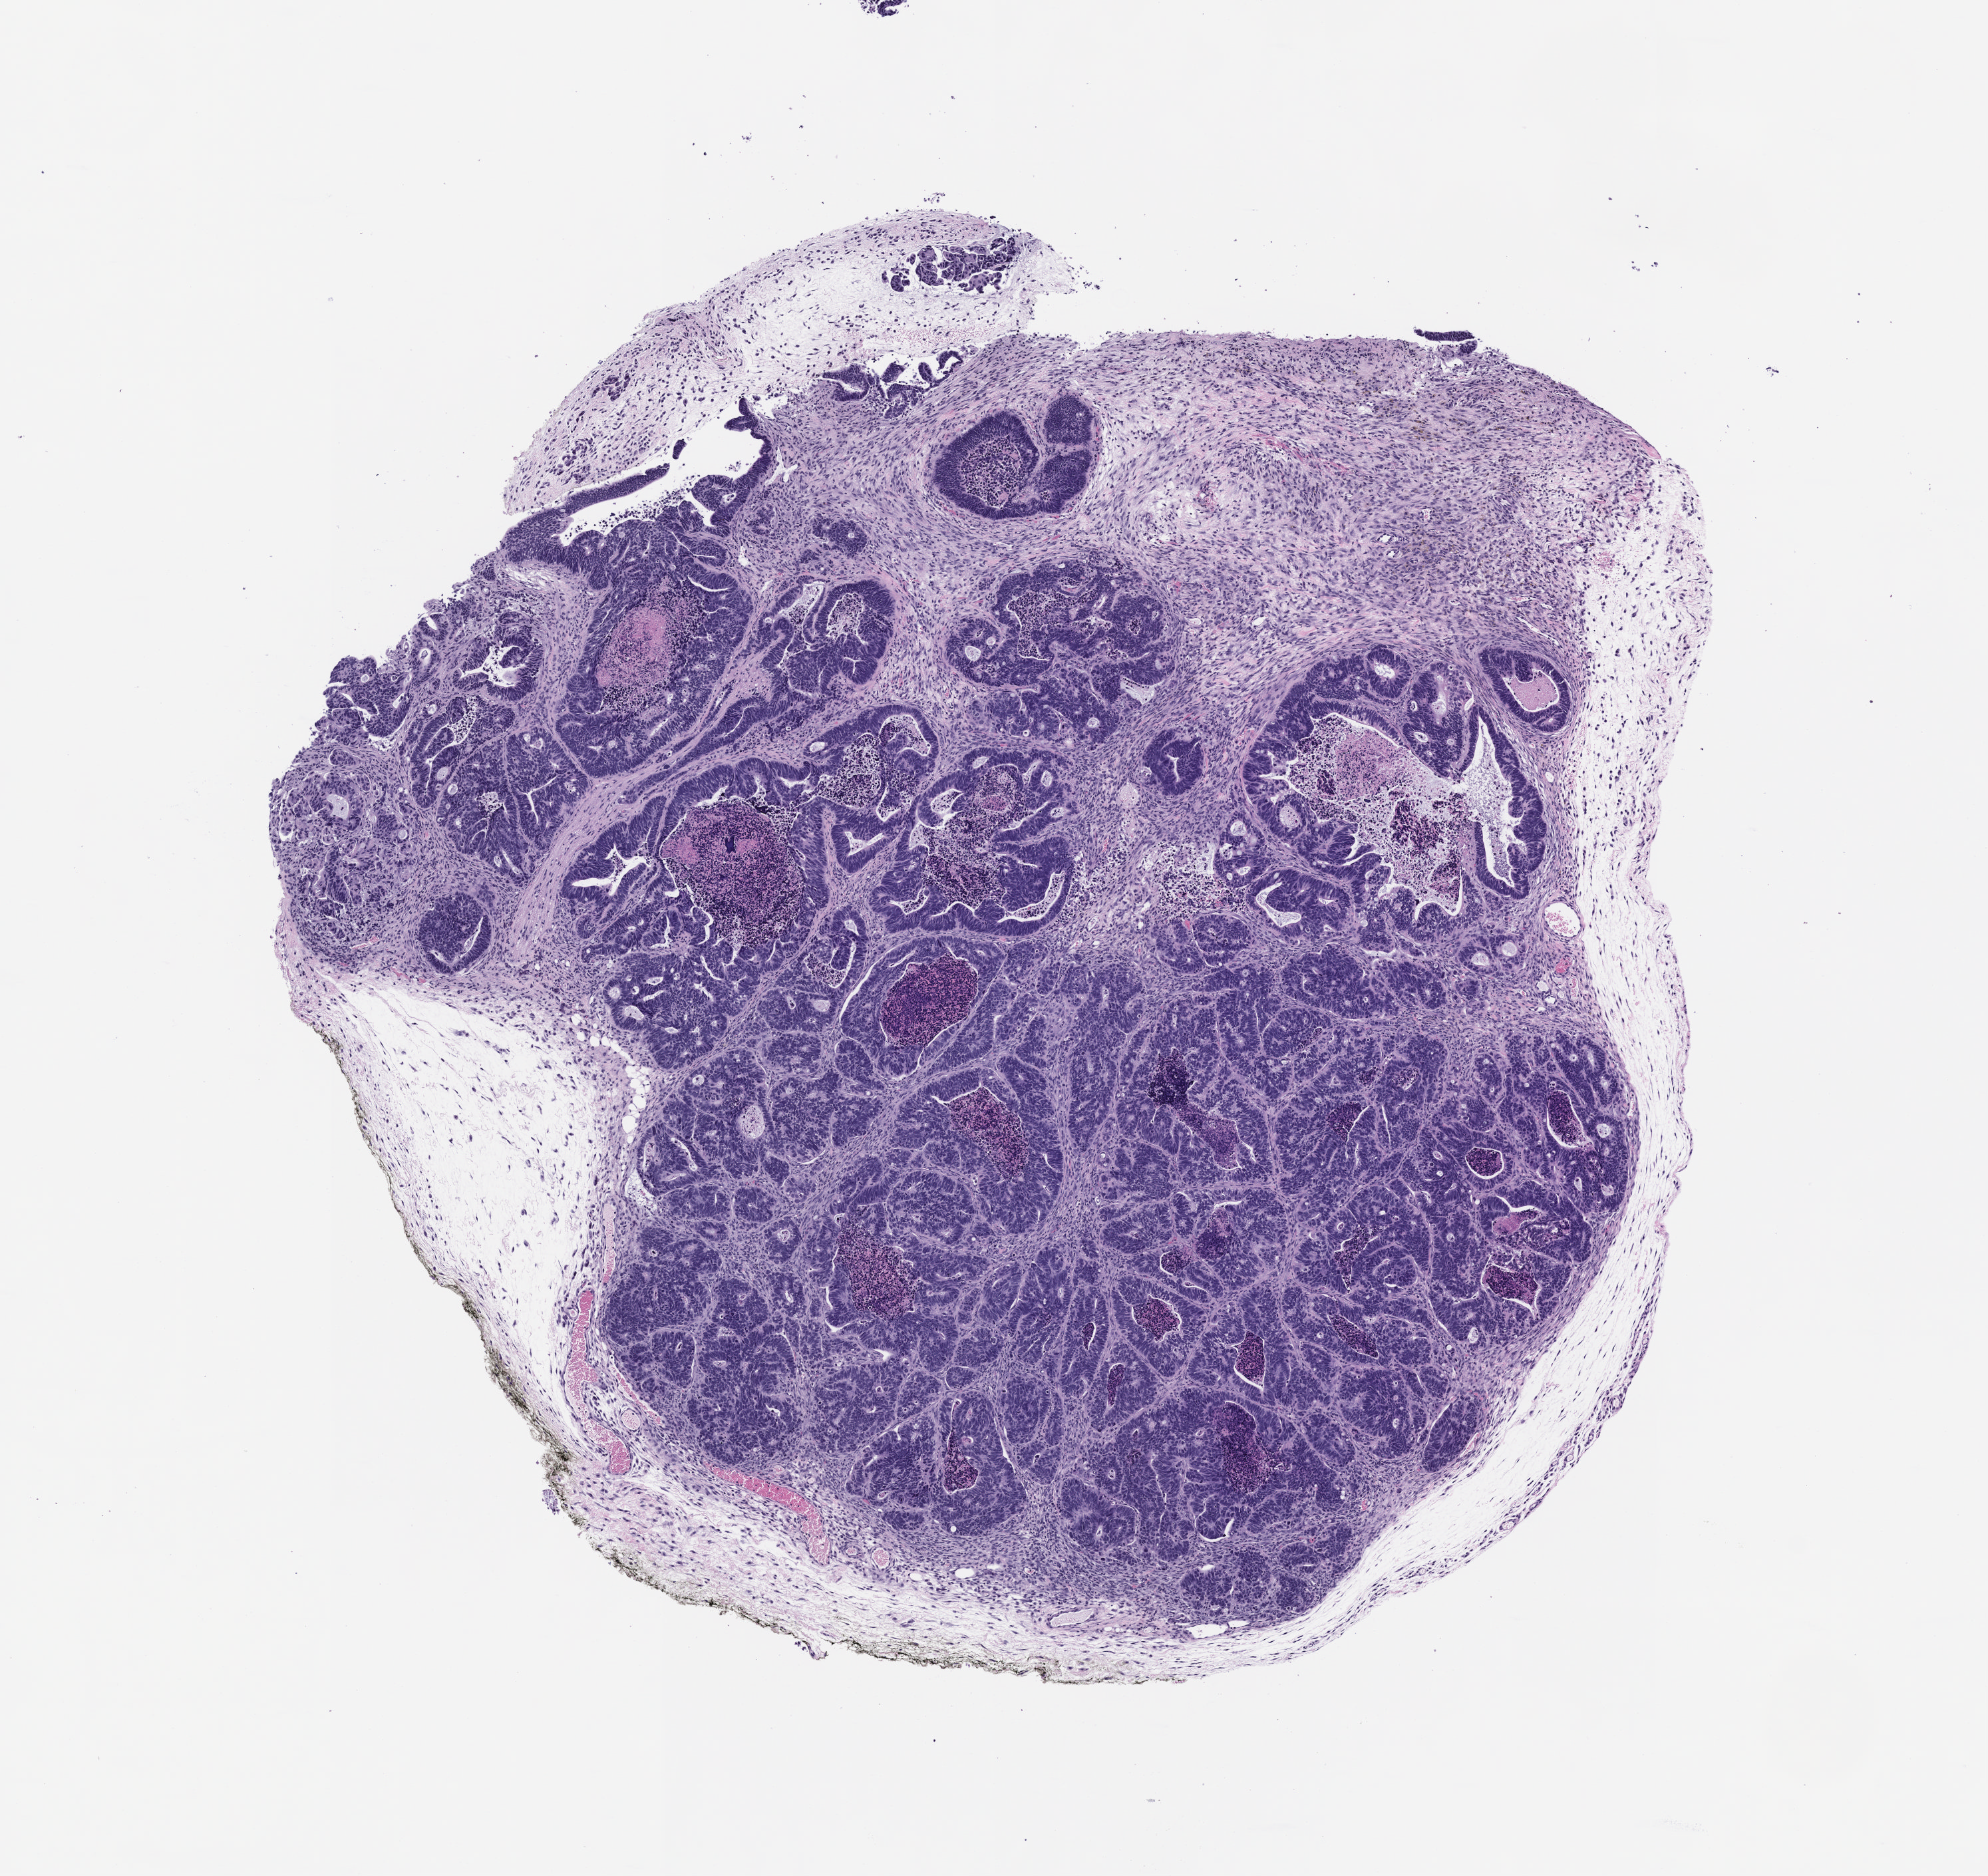
Hematoxylin and eosin (H&E) whole-slide image of a patient-derived xenograft (PDX) tumor grown in a mouse, passage 0 — a low-resolution overview of the entire scanned area, about 6.0 x 5.7 mm; formalin-fixed paraffin-embedded section; originating tumor site category: colon.
Originating patient diagnosis: Colon Adenocarcinoma.